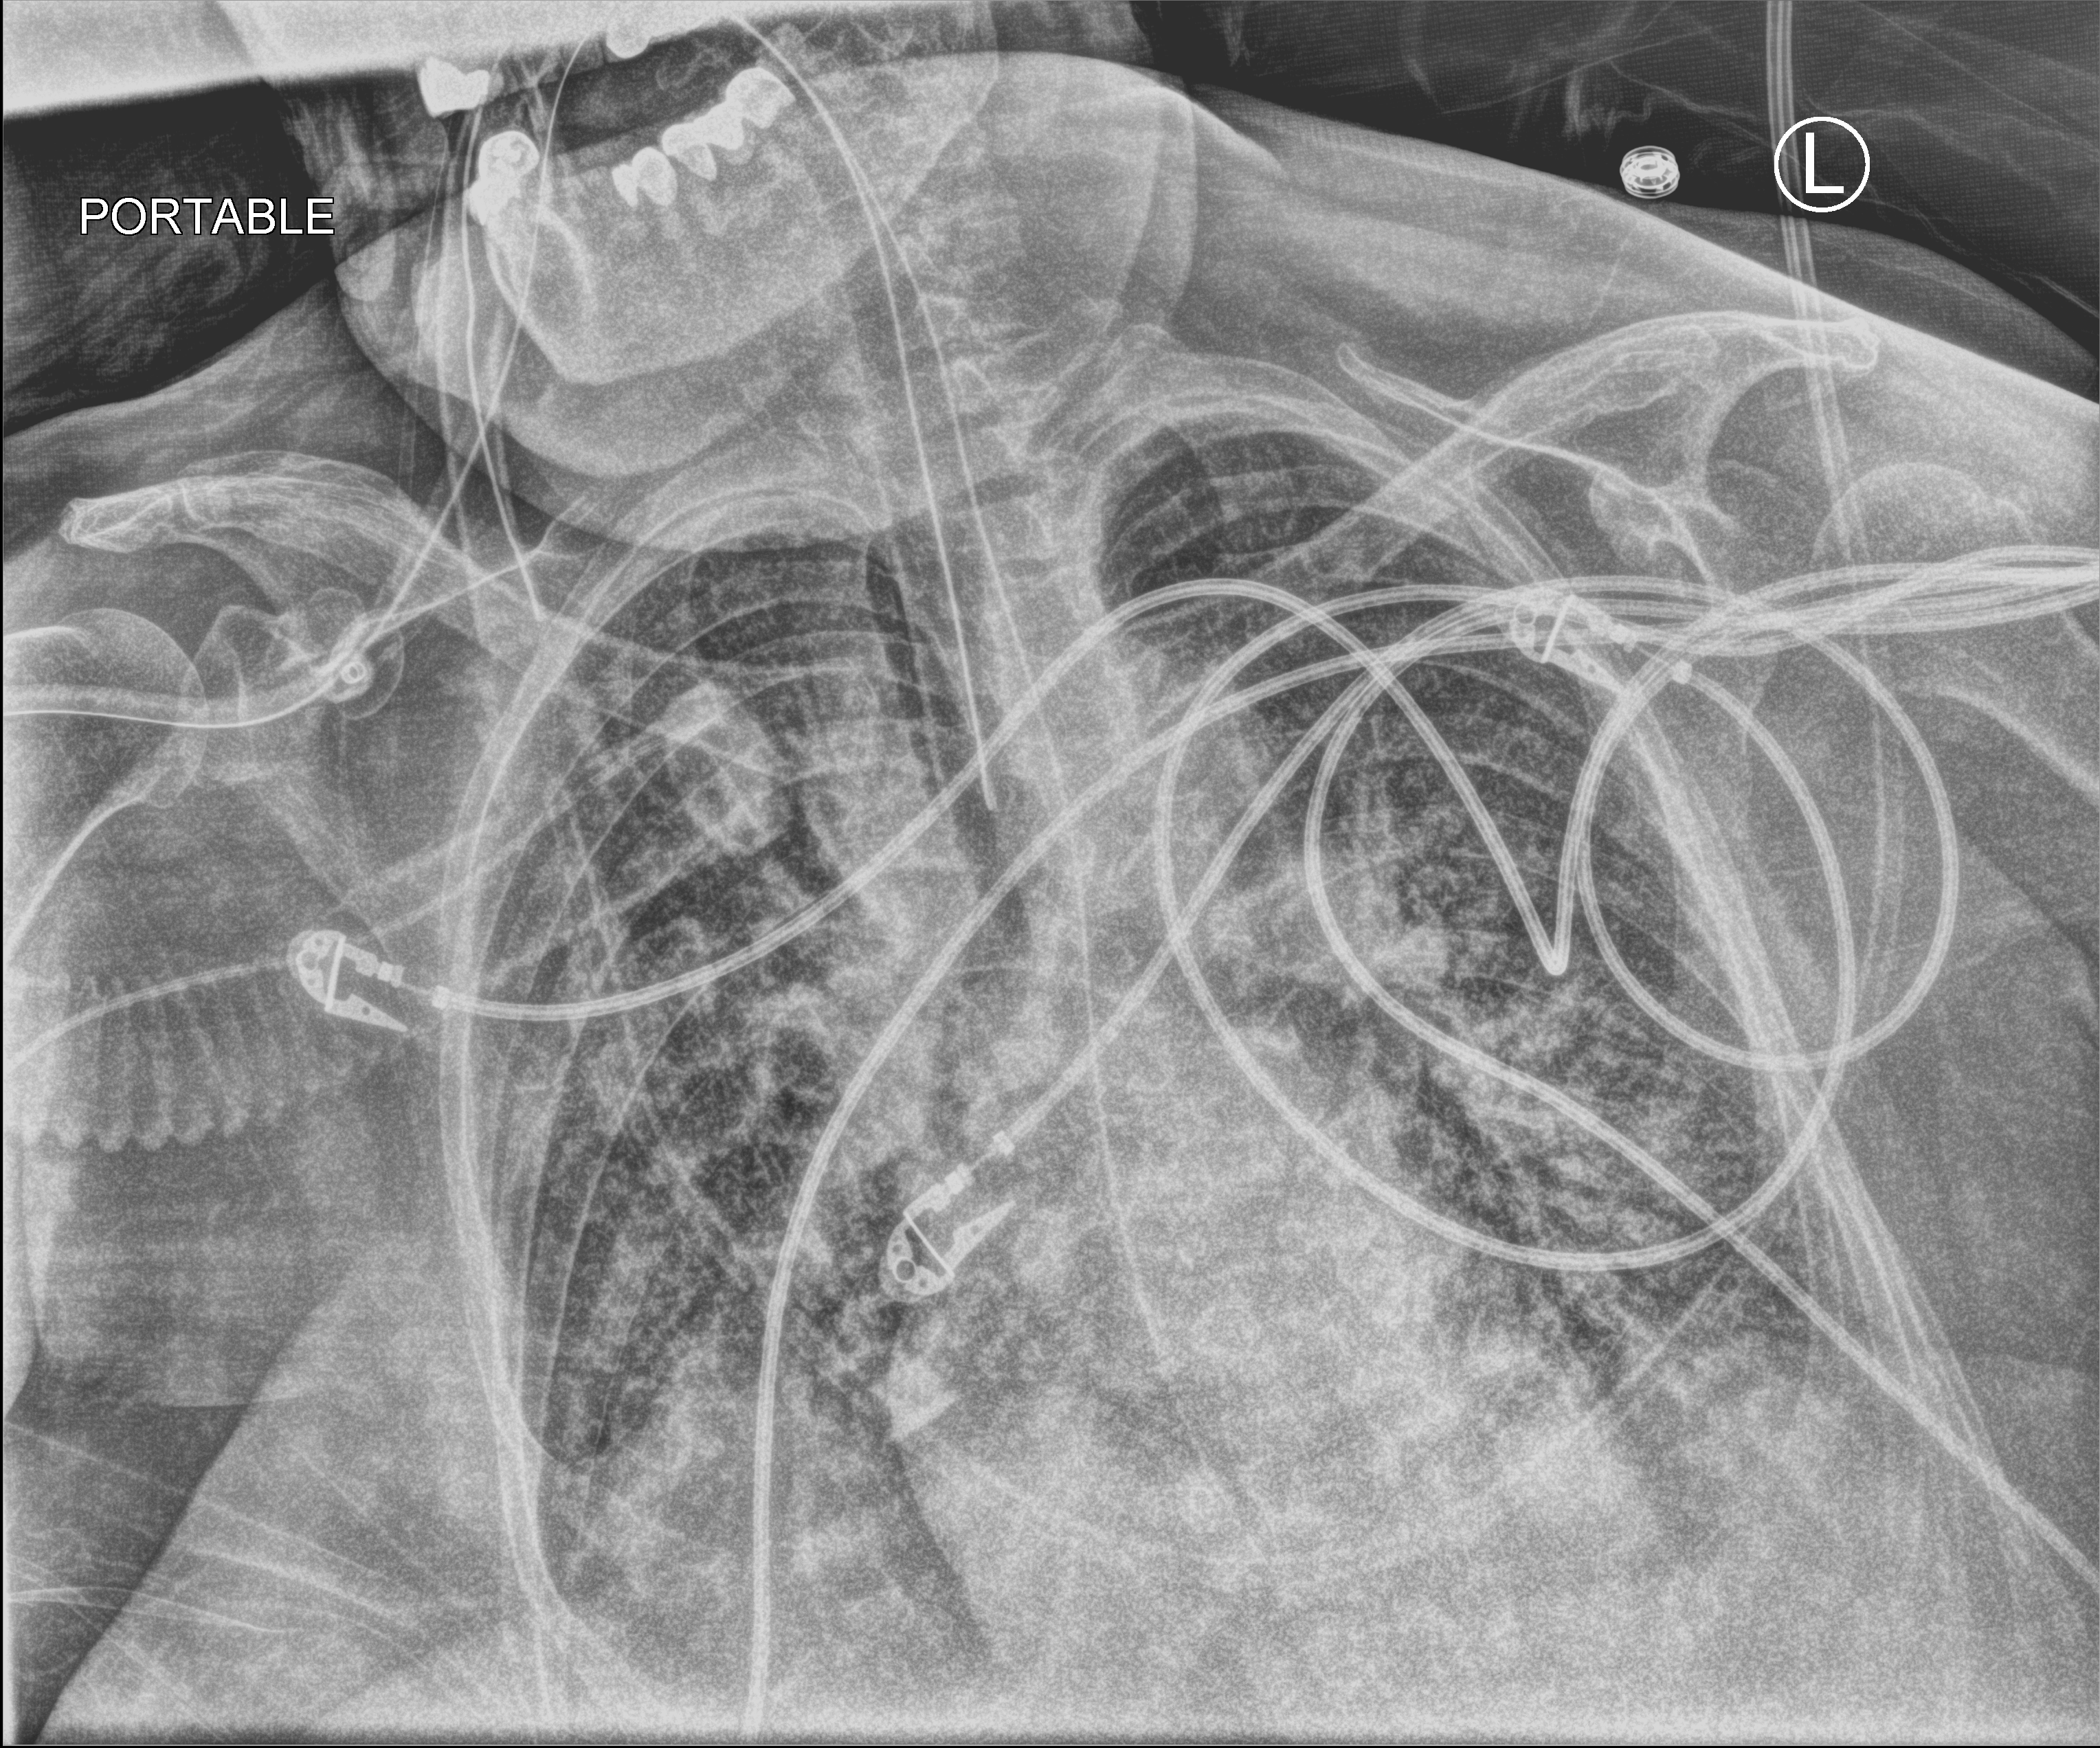
Chest X-ray (portable), anteroposterior (AP) projection. Patient hospitalised with COVID-19; female, aged 60–74 years.
Hospital-stay facts (about this admission, not read from this image; timing relative to this image not recorded):
- admitted to intensive care during this hospital stay: yes
- chronic kidney disease (admission record): no